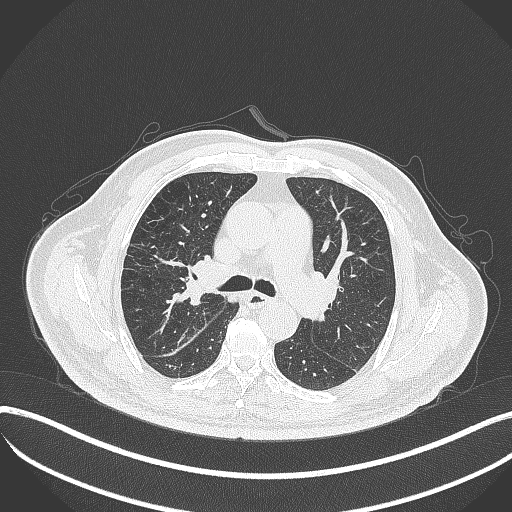
Chest CT, one axial slice. Position 231 of 401 along the scan axis. Reconstruction kernel B70f. Lung window (W 1500 / L -600 HU). 1 mm slice thickness. 512 × 512 image matrix, field of view 400 × 400 mm. Male patient, age 72 years. From the clinical record (not read from this slice): clinical TNM (as recorded): T1c N0 M0.
Outlined on this slice (bounding box drawn by a radiologist):
- lung tumour (recorded histology: squamous cell carcinoma): box from (x=176, y=260) to (x=211, y=309) px